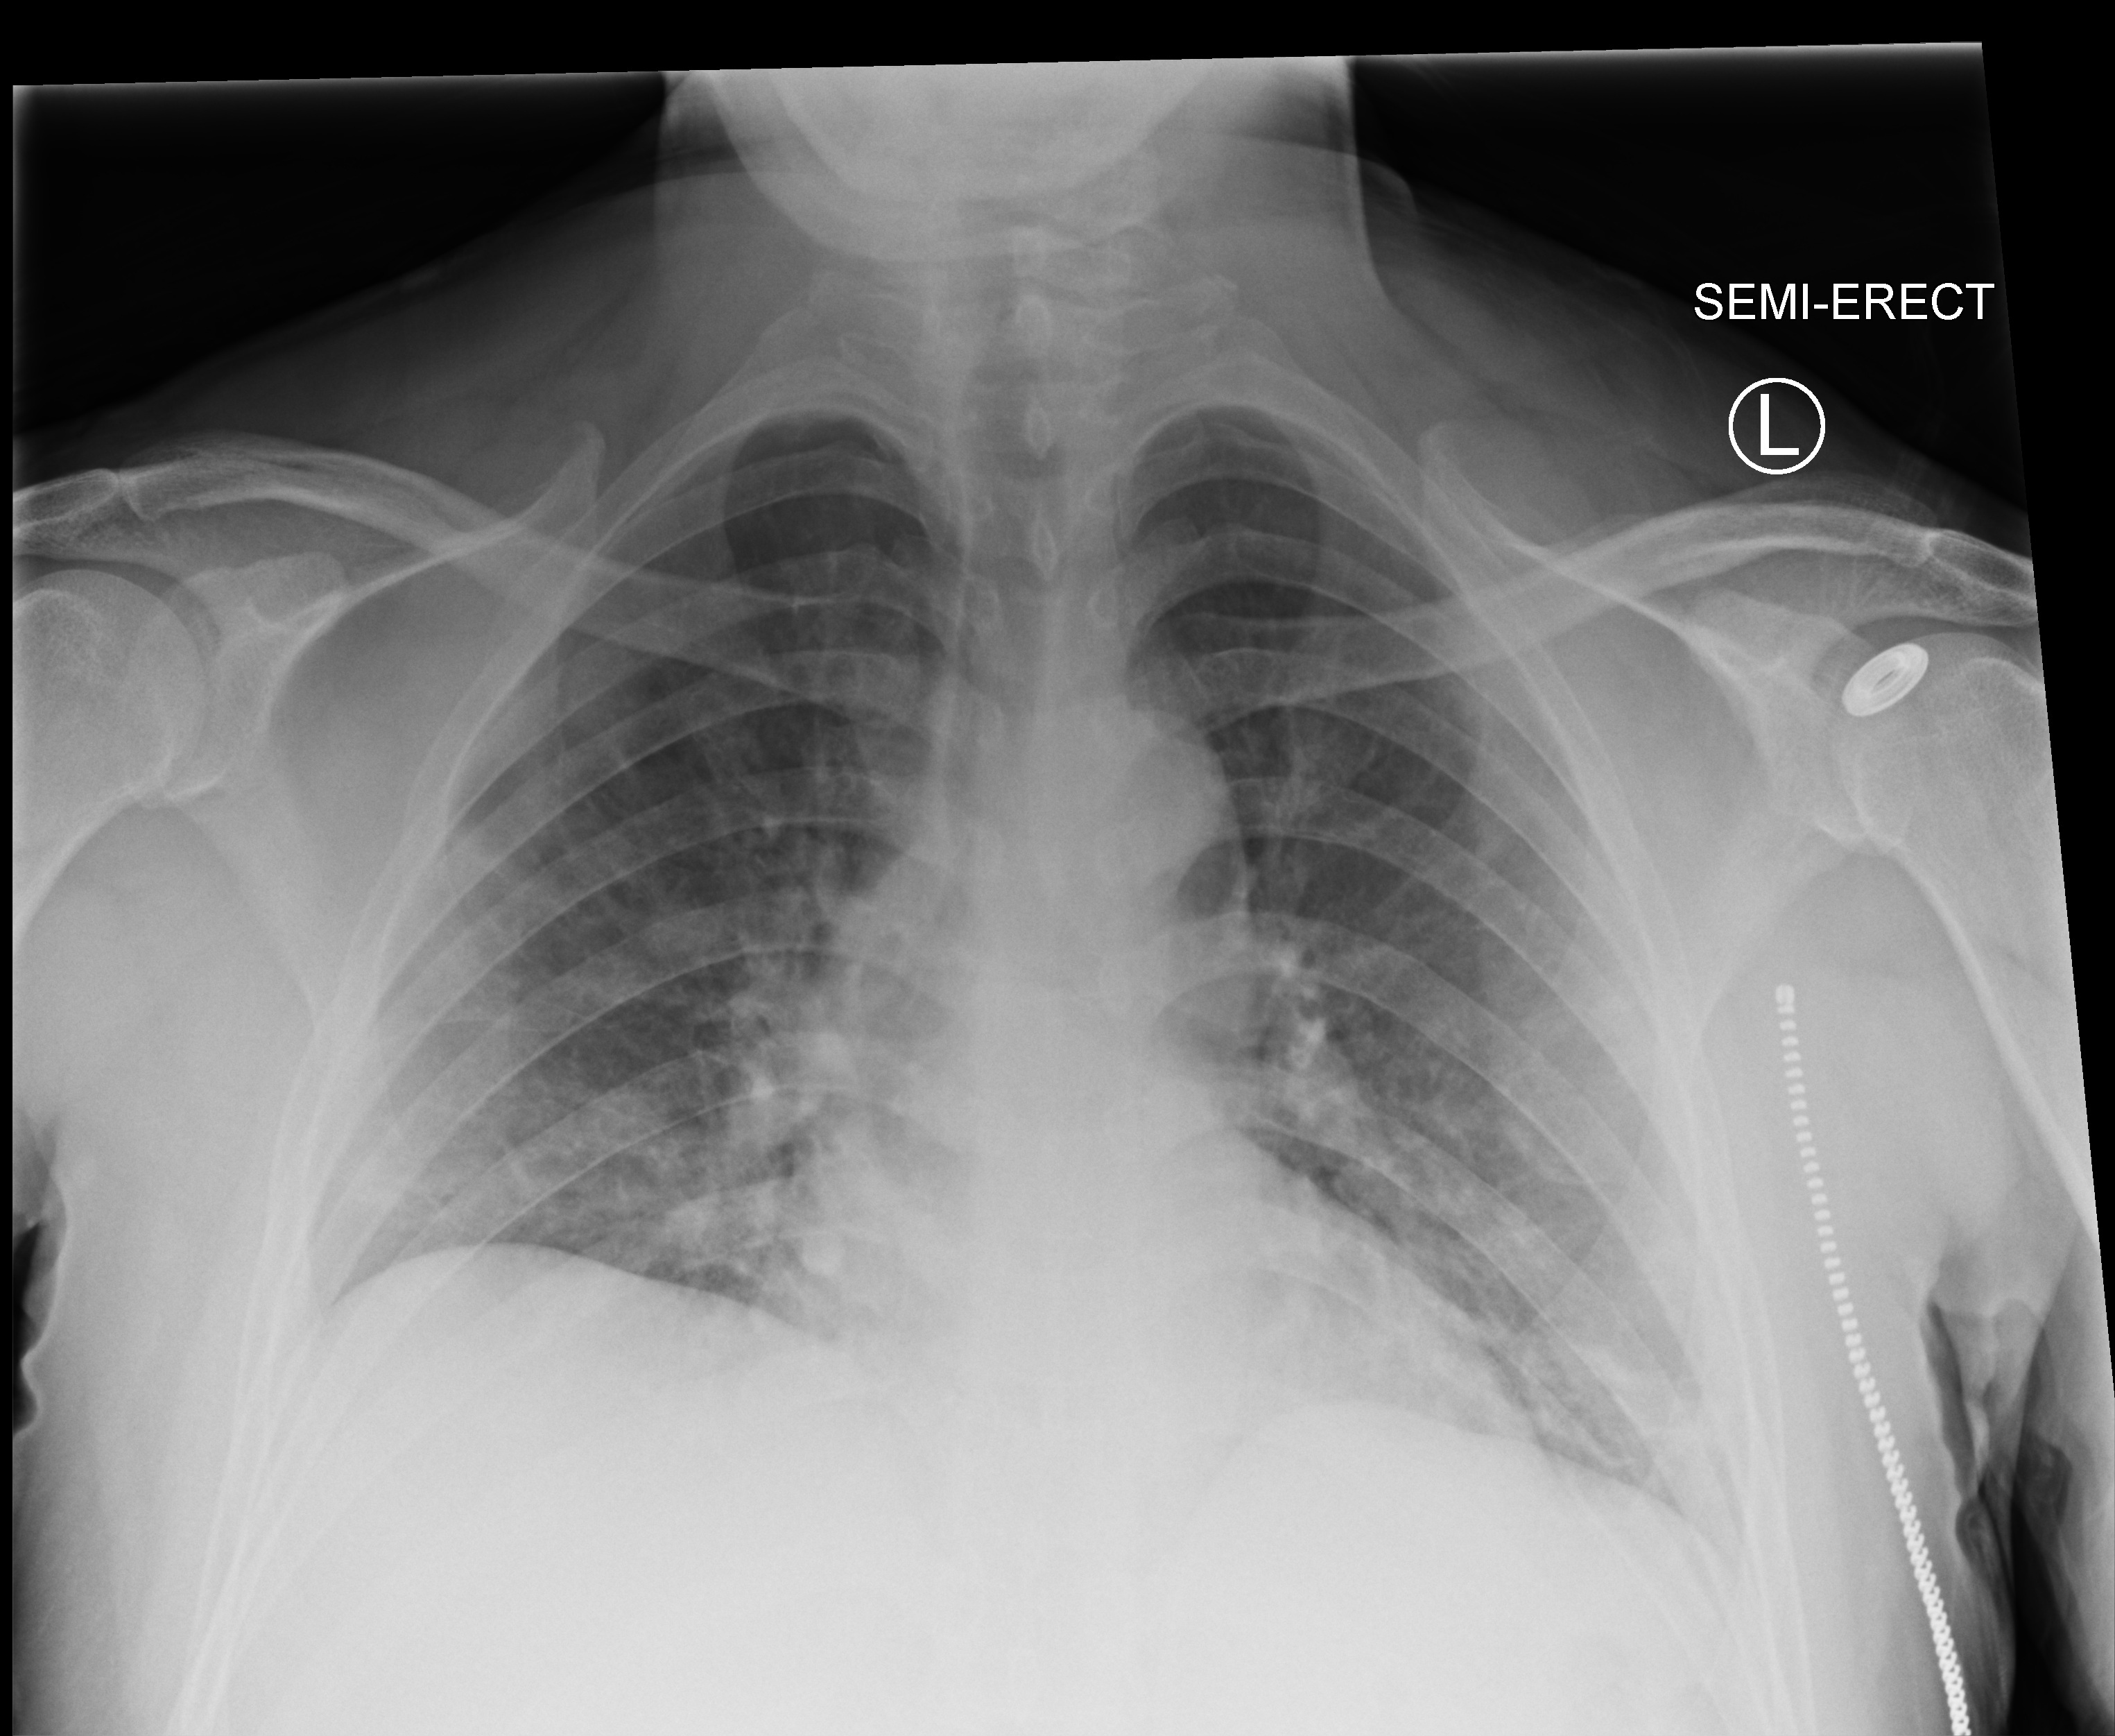
Chest X-ray (portable), anteroposterior (AP) projection. Patient hospitalised with COVID-19; male, aged 18–59 years.
Hospital-stay facts (about this admission, not read from this image; timing relative to this image not recorded): admitted to intensive care during this hospital stay: no; mechanically ventilated during this hospital stay: no.